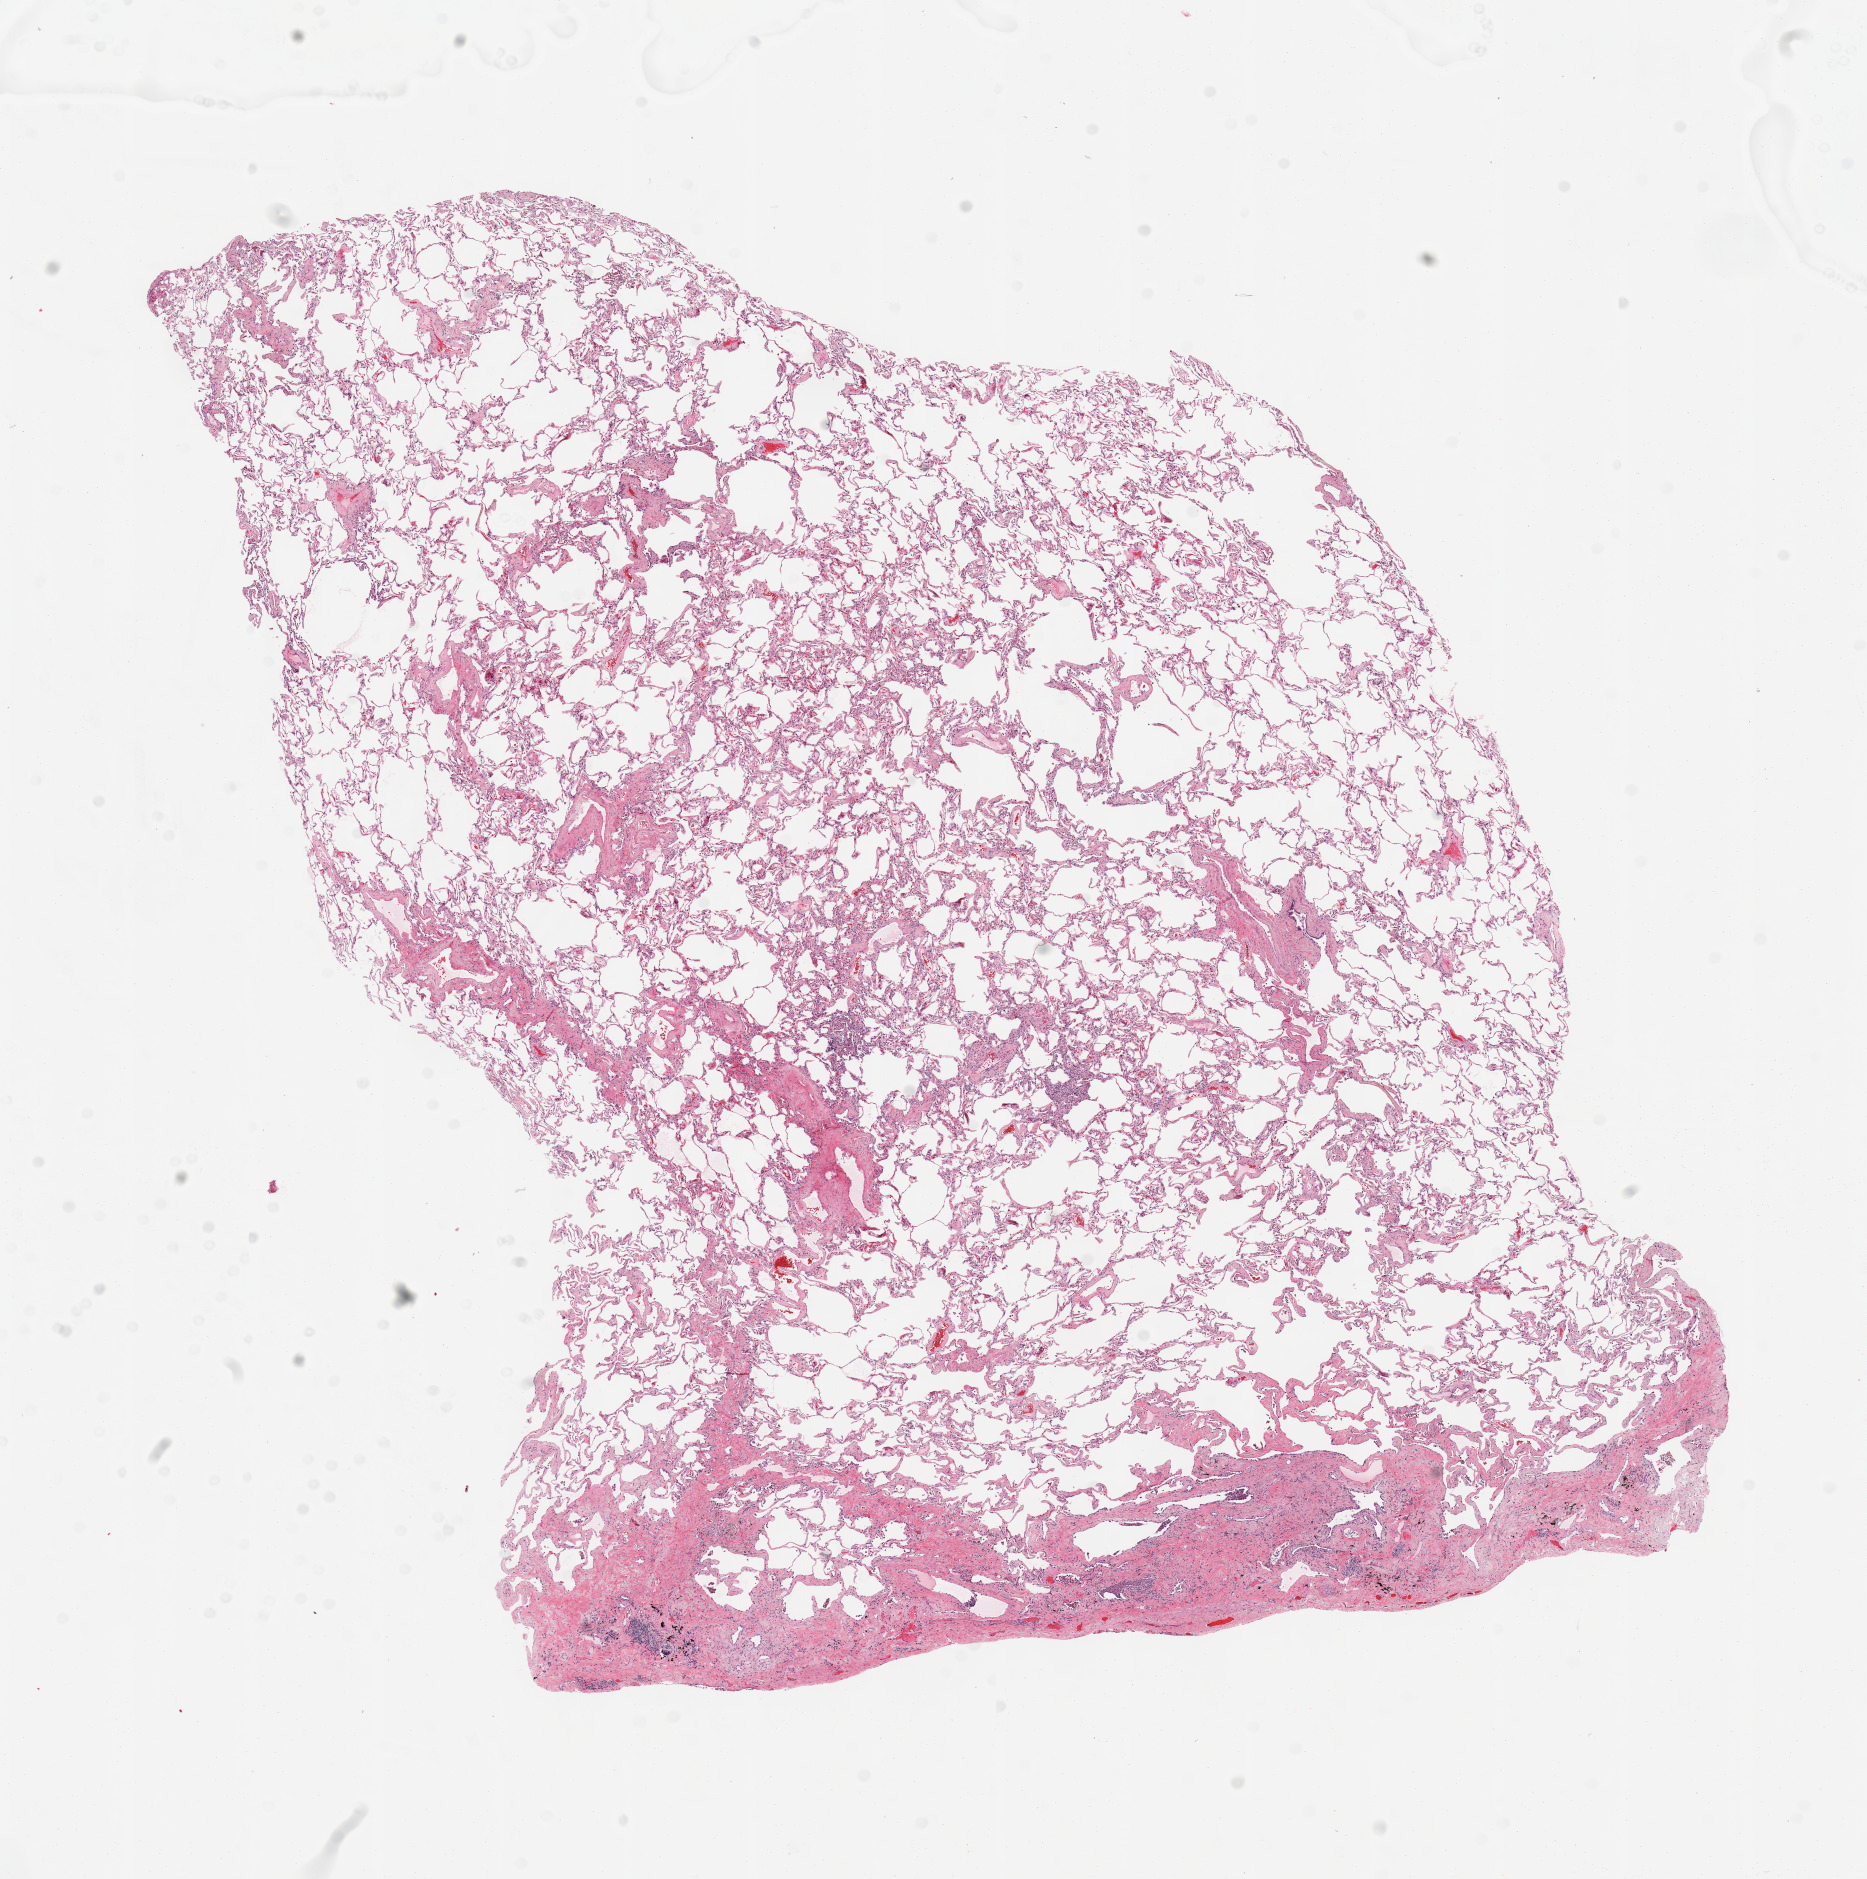
Whole-slide histology image, H&E — whole scanned area (about 14.8 x 14.9 mm, from a 20x scan) shown as a low-resolution overview, normal (non-tumour) tissue sample, sampled site: lung. Patient: male, age 70 years.
This section: normal (non-tumour) tissue from the same patient. Patient diagnosis: Adenocarcinoma, NOS.